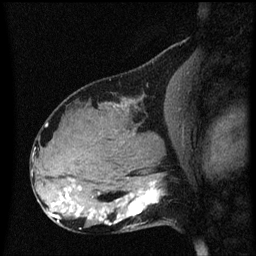
Breast MRI (dynamic contrast-enhanced), one sagittal slice; slice 28 of 60 in the series (ordered by position); dynamic contrast-enhanced series, image 2 of 3 at this slice position (ordered by acquisition); 1.5 T; TE 4.2 ms, TR 8.4 ms; 2 mm slice thickness; 256 × 256 image matrix, field of view 200 × 200 mm. Patient: female, 31 years. Case-level facts recorded for this patient, not image findings: setting: breast cancer imaged before/during neoadjuvant chemotherapy; receptor status: HR-positive, HER2-negative.
Outlined on this slice (semi-automatically segmented with operator editing):
- analysis volume of interest (the breast-tissue region the enhancement analysis was run in; not a lesion): bounding box (x1, y1, x2, y2) in pixels: (102, 166, 173, 229)
- tumour enhancement mask (voxels above the 70 % enhancement threshold inside the analysis volume of interest): (102, 182, 160, 225)